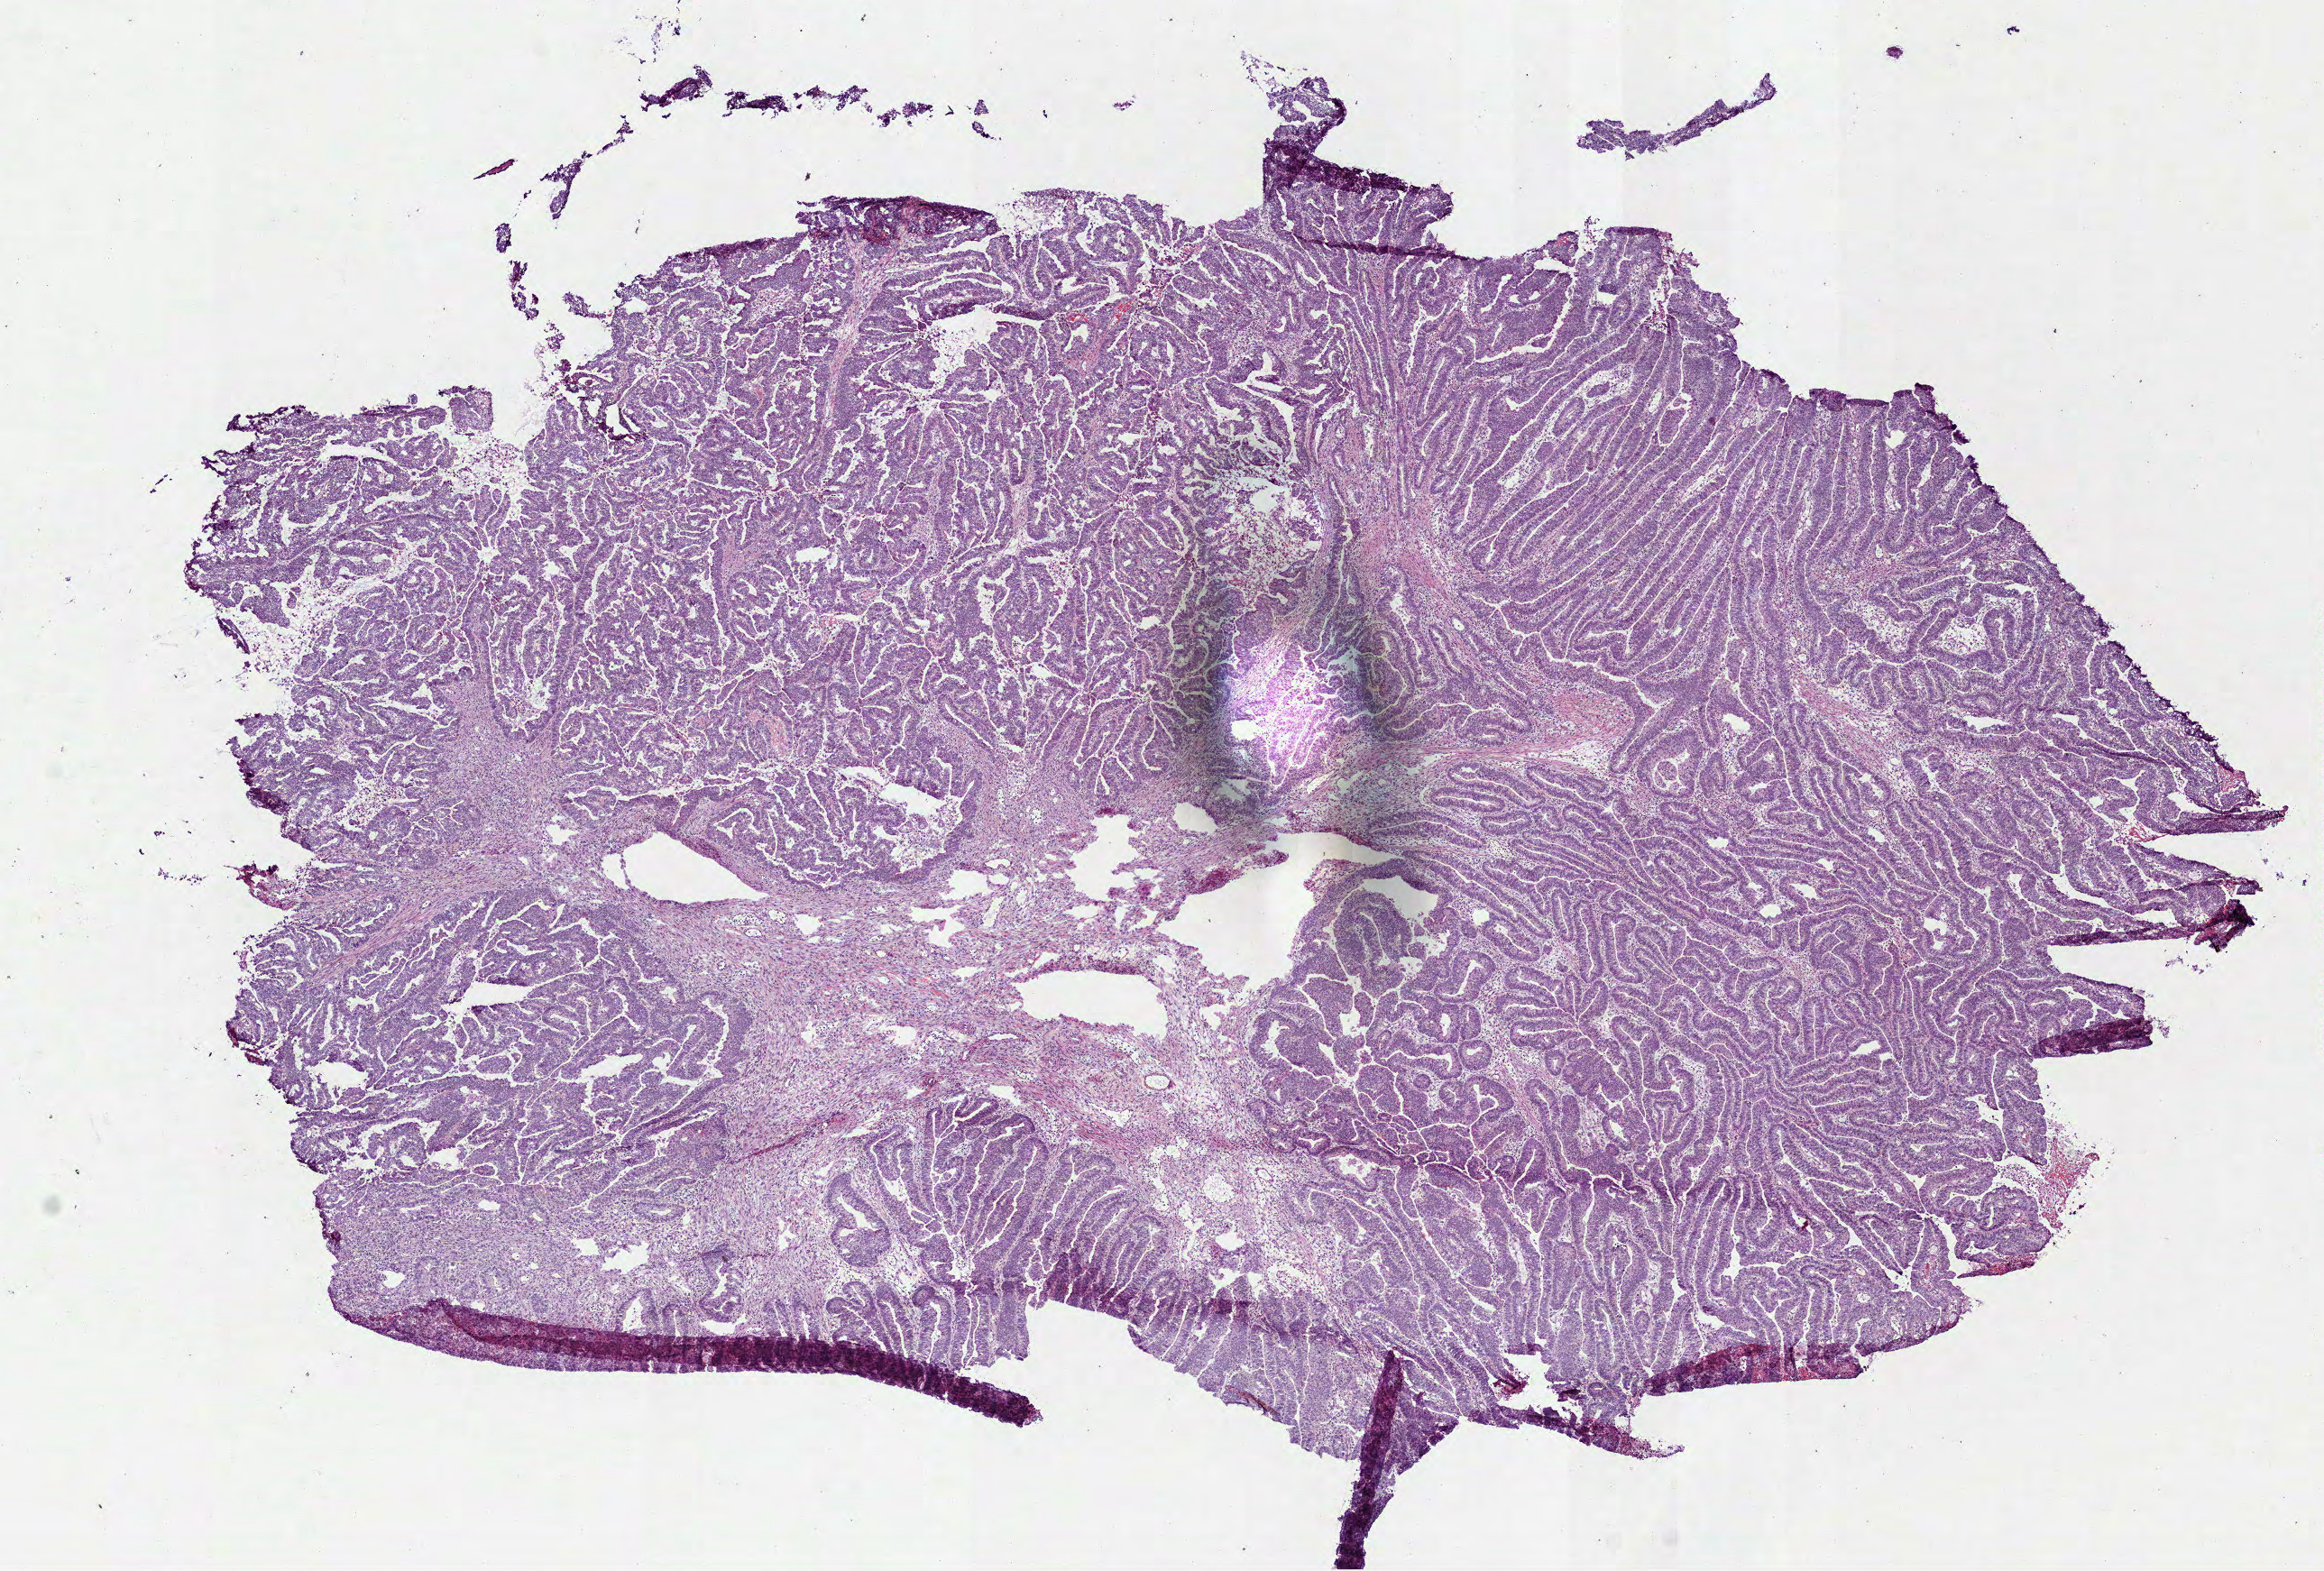
Whole-slide histology image, Hematoxylin and eosin (H&E) stained — shown as a low-resolution overview of the whole scanned area (about 10.4 x 7.0 mm, slide scanned at 40x); frozen section; colon, primary tumour sample. Male patient; age at initial diagnosis 64 years. Pathologist review of this section (percent, as recorded): tumour cells 100%, tumour nuclei 90%, normal cells 0%, stromal cells 0%, necrosis 0%. Infiltration values recorded for this section: lymphocyte infiltration 2%, monocyte infiltration 1%, neutrophil infiltration 1%.
• pathologic diagnosis: Adenocarcinoma, NOS
• AJCC pathologic stage: IIIB (7th edition)